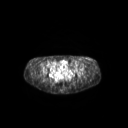
FDG PET of an extremity soft-tissue mass (from a PET/CT study), one axial slice; slice 80 of 267 in the series (ordered by position); 3.27 mm slice thickness; 128 × 128 image matrix, field of view 600 × 600 mm. Patient: female, 24 years. From the clinical record (not read from this slice): histological type: leiomyosarcoma; grade: high; site of the primary tumour: groin.
Outlined on this slice (expert contour drawn on MRI and transferred to this co-registered scan by the dataset authors):
- gross tumour volume including surrounding oedema: bounding box <77,60,92,64> (left, top, right, bottom; pixels)